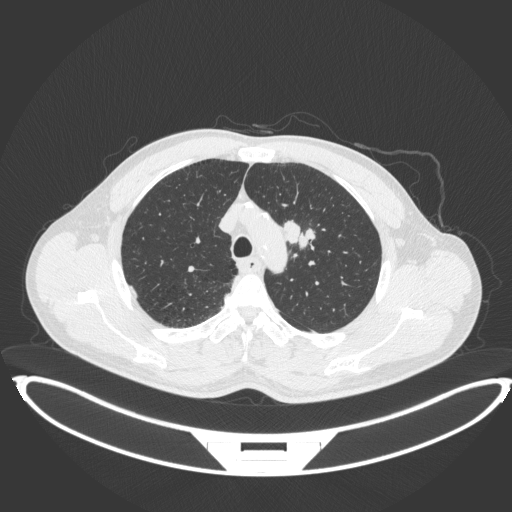
Chest CT, one axial slice. Slice 334 of 407 in the series (ordered by position). Reconstruction kernel B31f. 120 kVp. Lung window (W 1500 / L -600 HU). 1 mm slice thickness. 512 × 512 image matrix, field of view 457 × 457 mm. Male patient, age 60 years. Case-level facts recorded for this patient, not image findings: clinical TNM (as recorded): T2a N0 M0.
Annotated regions visible in this slice (bounding box drawn by a radiologist):
- lung tumour (recorded histology: squamous cell carcinoma): box from (x=281, y=216) to (x=318, y=251) px